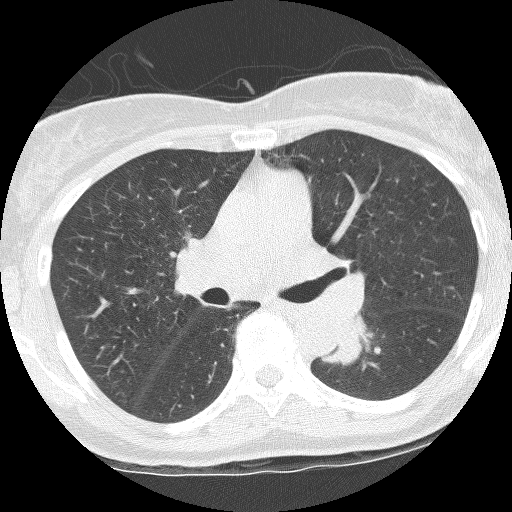
Low-dose screening chest CT, axial slice, third screening round (two years after baseline), lung window (W 1500 / L -600 HU), 2.5 mm slice thickness, slice 50 of 115 in the series. Female participant, aged 62 years at enrolment. Former smoker at enrolment.
• Expert-annotated lung lesion, bounding box [x1, y1, x2, y2] px = [323, 323, 385, 365].
• The screening reader recorded 3 non-calcified nodules or masses ≥4 mm on this exam (right upper lobe, left lower lobe, left upper lobe); which of them this box marks is not recorded.
• Later outcome: lung cancer diagnosed 165 days after this screen — squamous cell carcinoma, NOS, left lower lobe, stage IIIB (AJCC 6th edition), 31 mm at pathology.